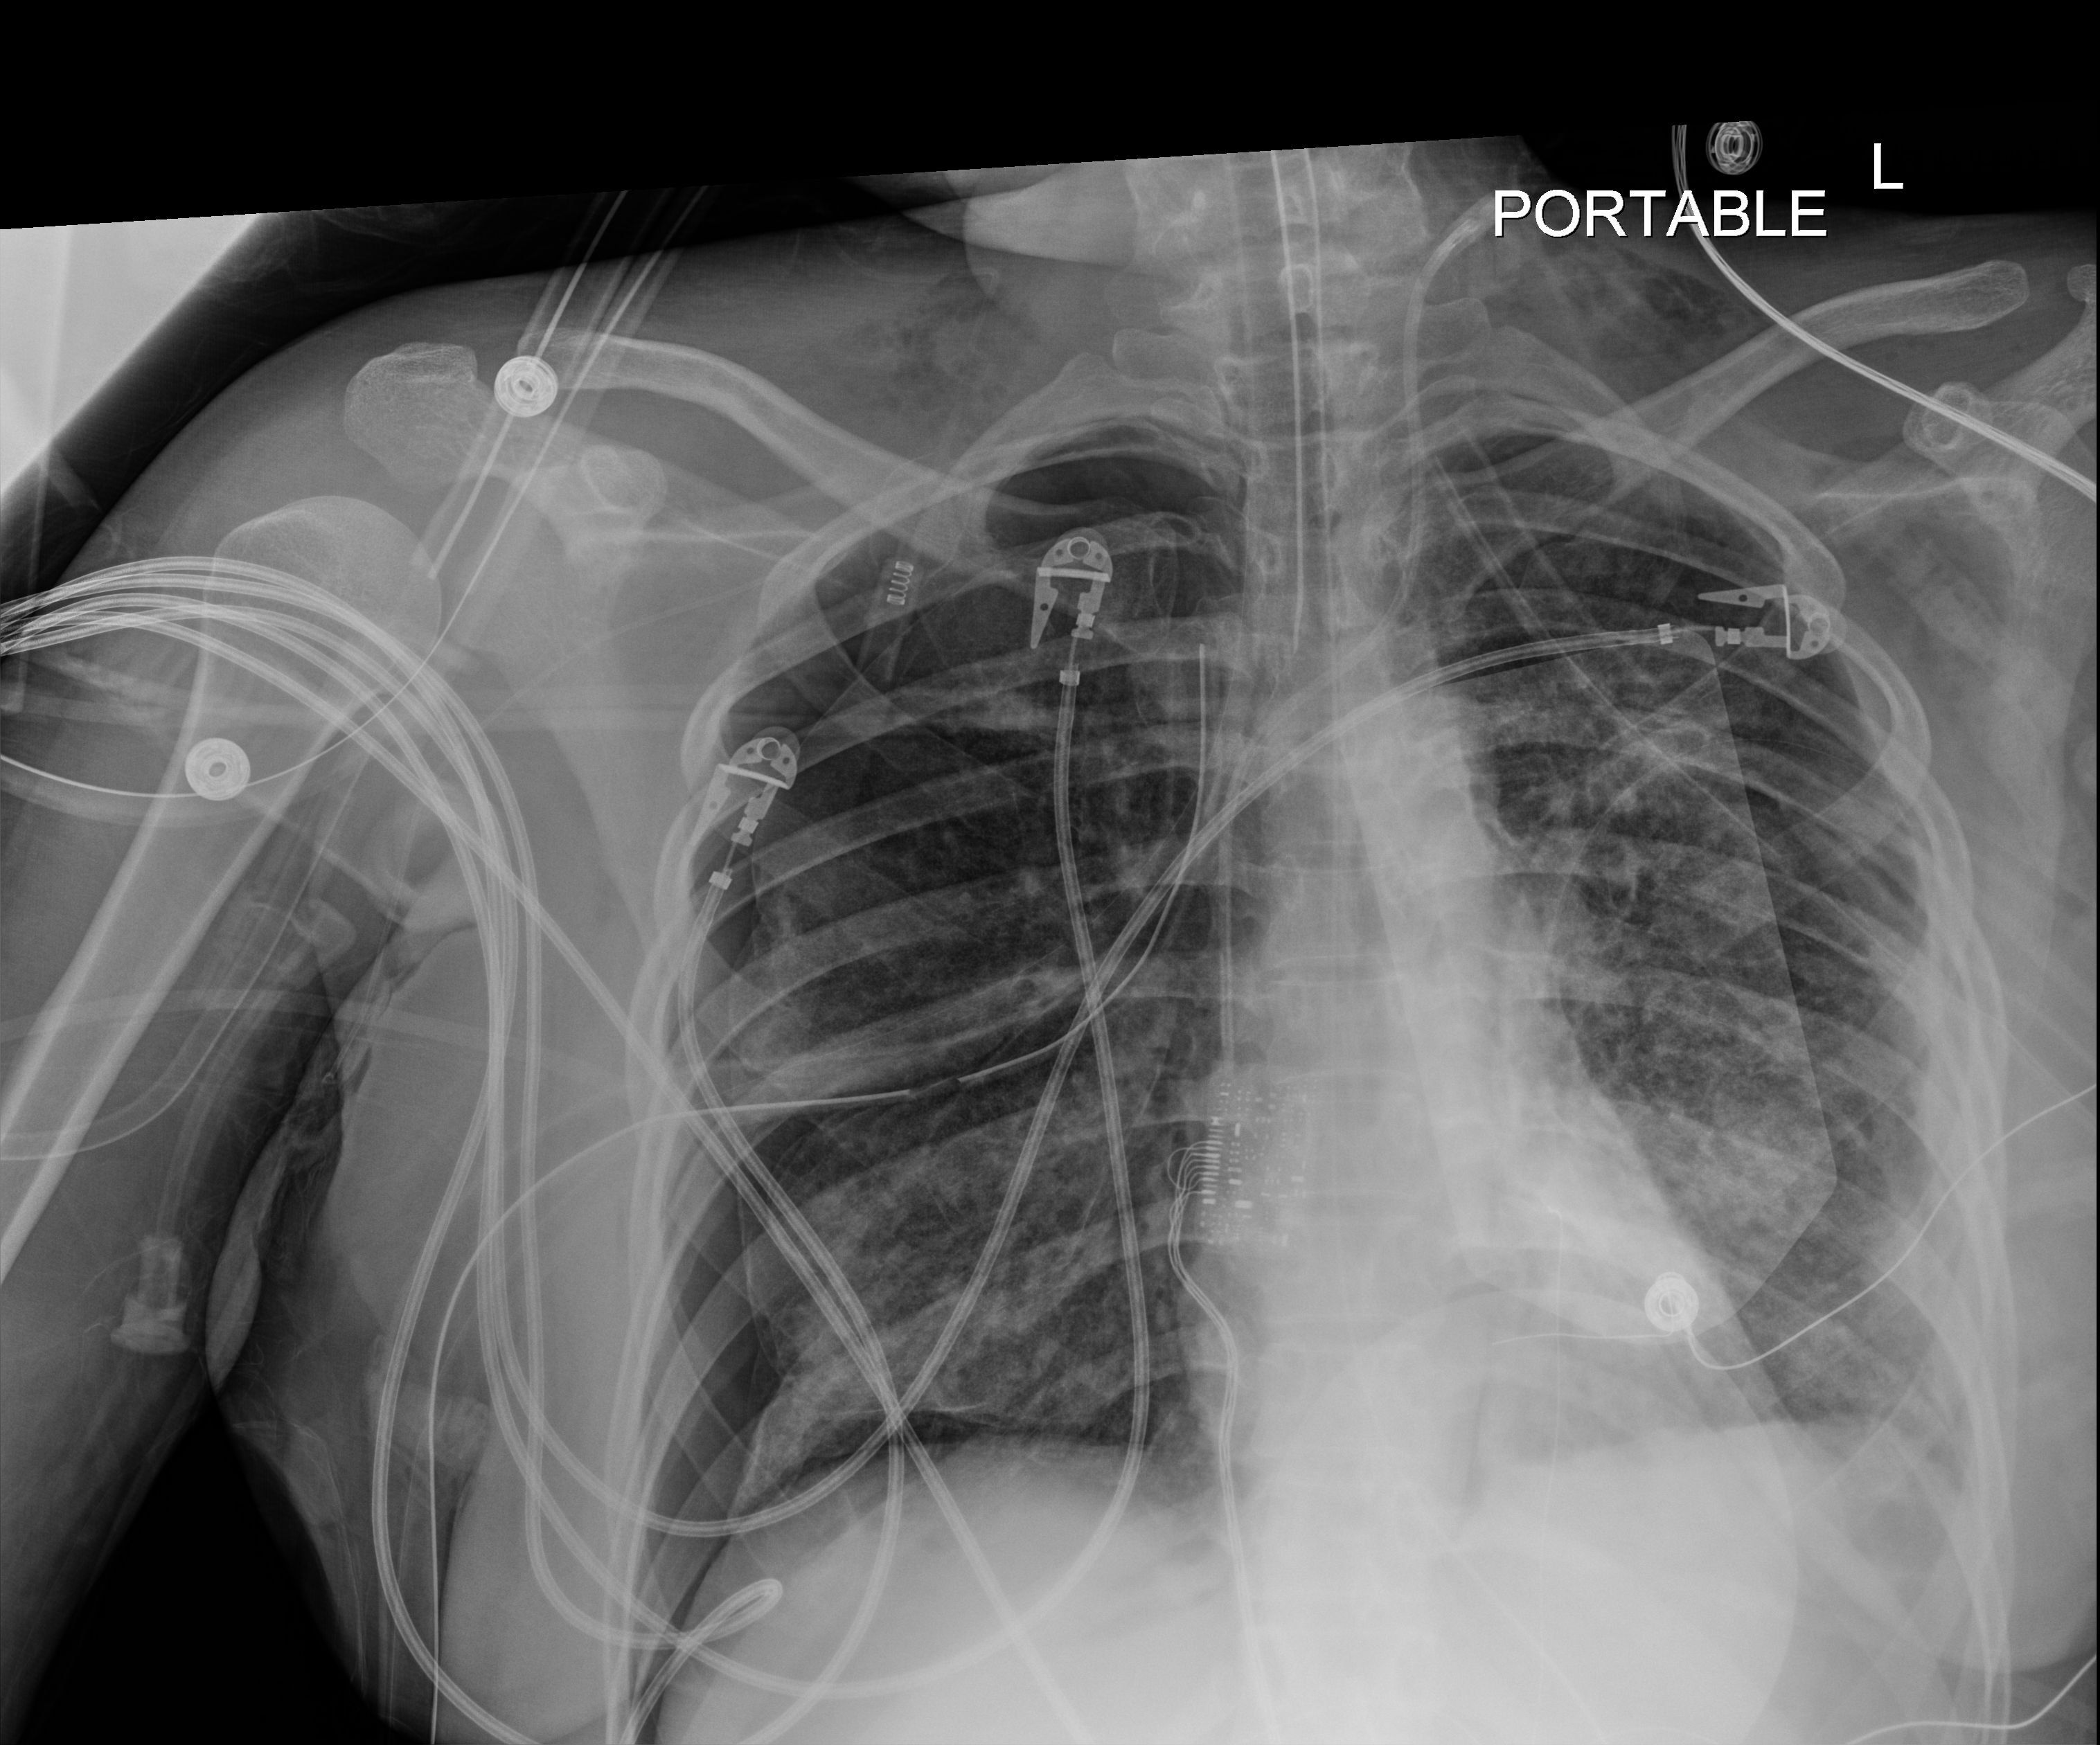
Bedside chest radiograph (digital radiography); anteroposterior (AP) projection. Adult patient hospitalised with COVID-19, age 18–59 years.
Hospital-stay facts (about this admission, not read from this image; timing relative to this image not recorded):
- admitted to intensive care during this hospital stay: yes
- diabetes (admission record): no